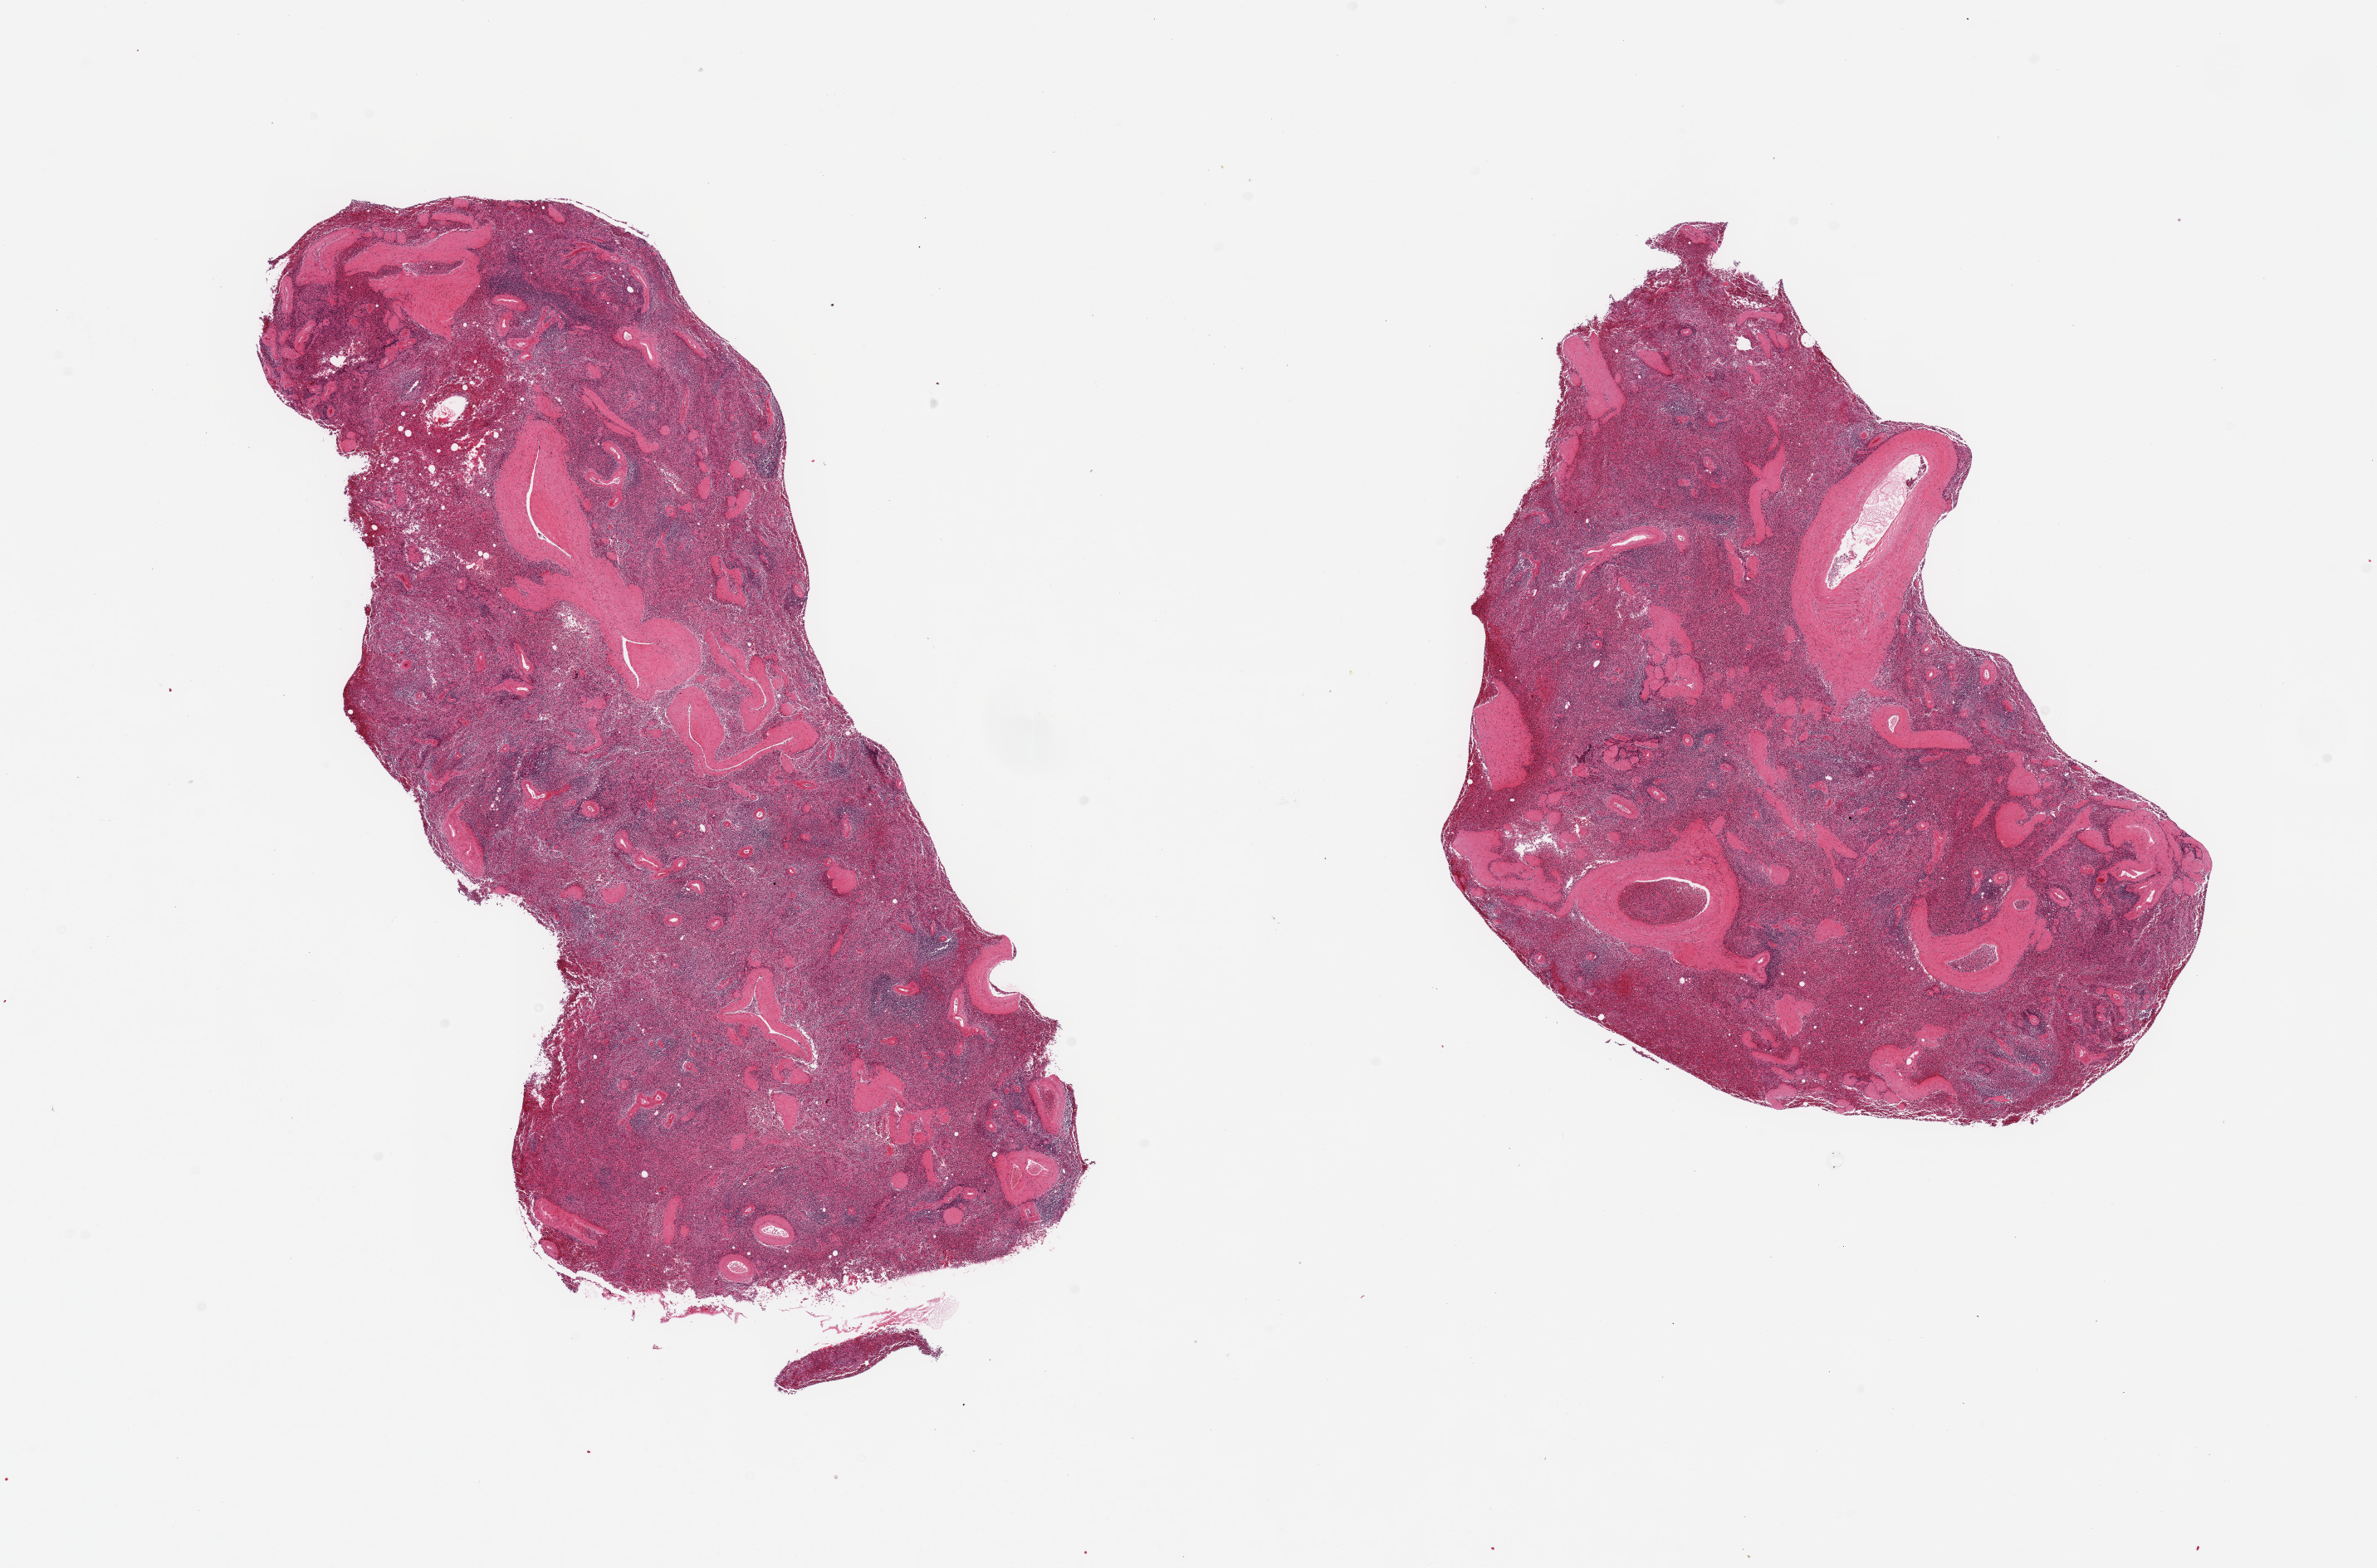
Digitized haematoxylin and eosin-stained section — shown as a low-resolution overview of the whole scanned area (about 22.6 x 14.9 mm), PAXgene-fixed, paraffin-embedded tissue, section of spleen (target tissue), tissue donor sample.
- reviewer comment on this tissue sample: 2 pieces; high fibrovascular content